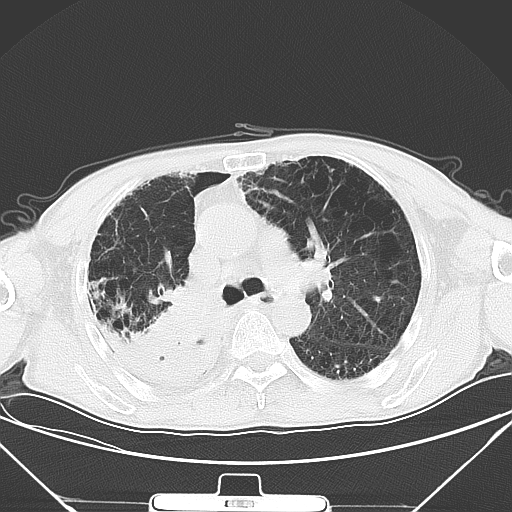
Chest CT, one axial slice. Slice 31 of 50 in the series (ordered by position). 120 kVp. Lung window (W 1500 / L -600 HU). 5 mm slice thickness. 512 × 512 image matrix, field of view 373 × 373 mm. Male patient, age 65 years. Case-level facts recorded for this patient, not image findings: clinical TNM (as recorded): T3 N1 M1a.
Structures marked on this image (bounding box drawn by a radiologist):
- lung tumour (recorded histology: squamous cell carcinoma): bounding box <139,293,233,374> (left, top, right, bottom; pixels)